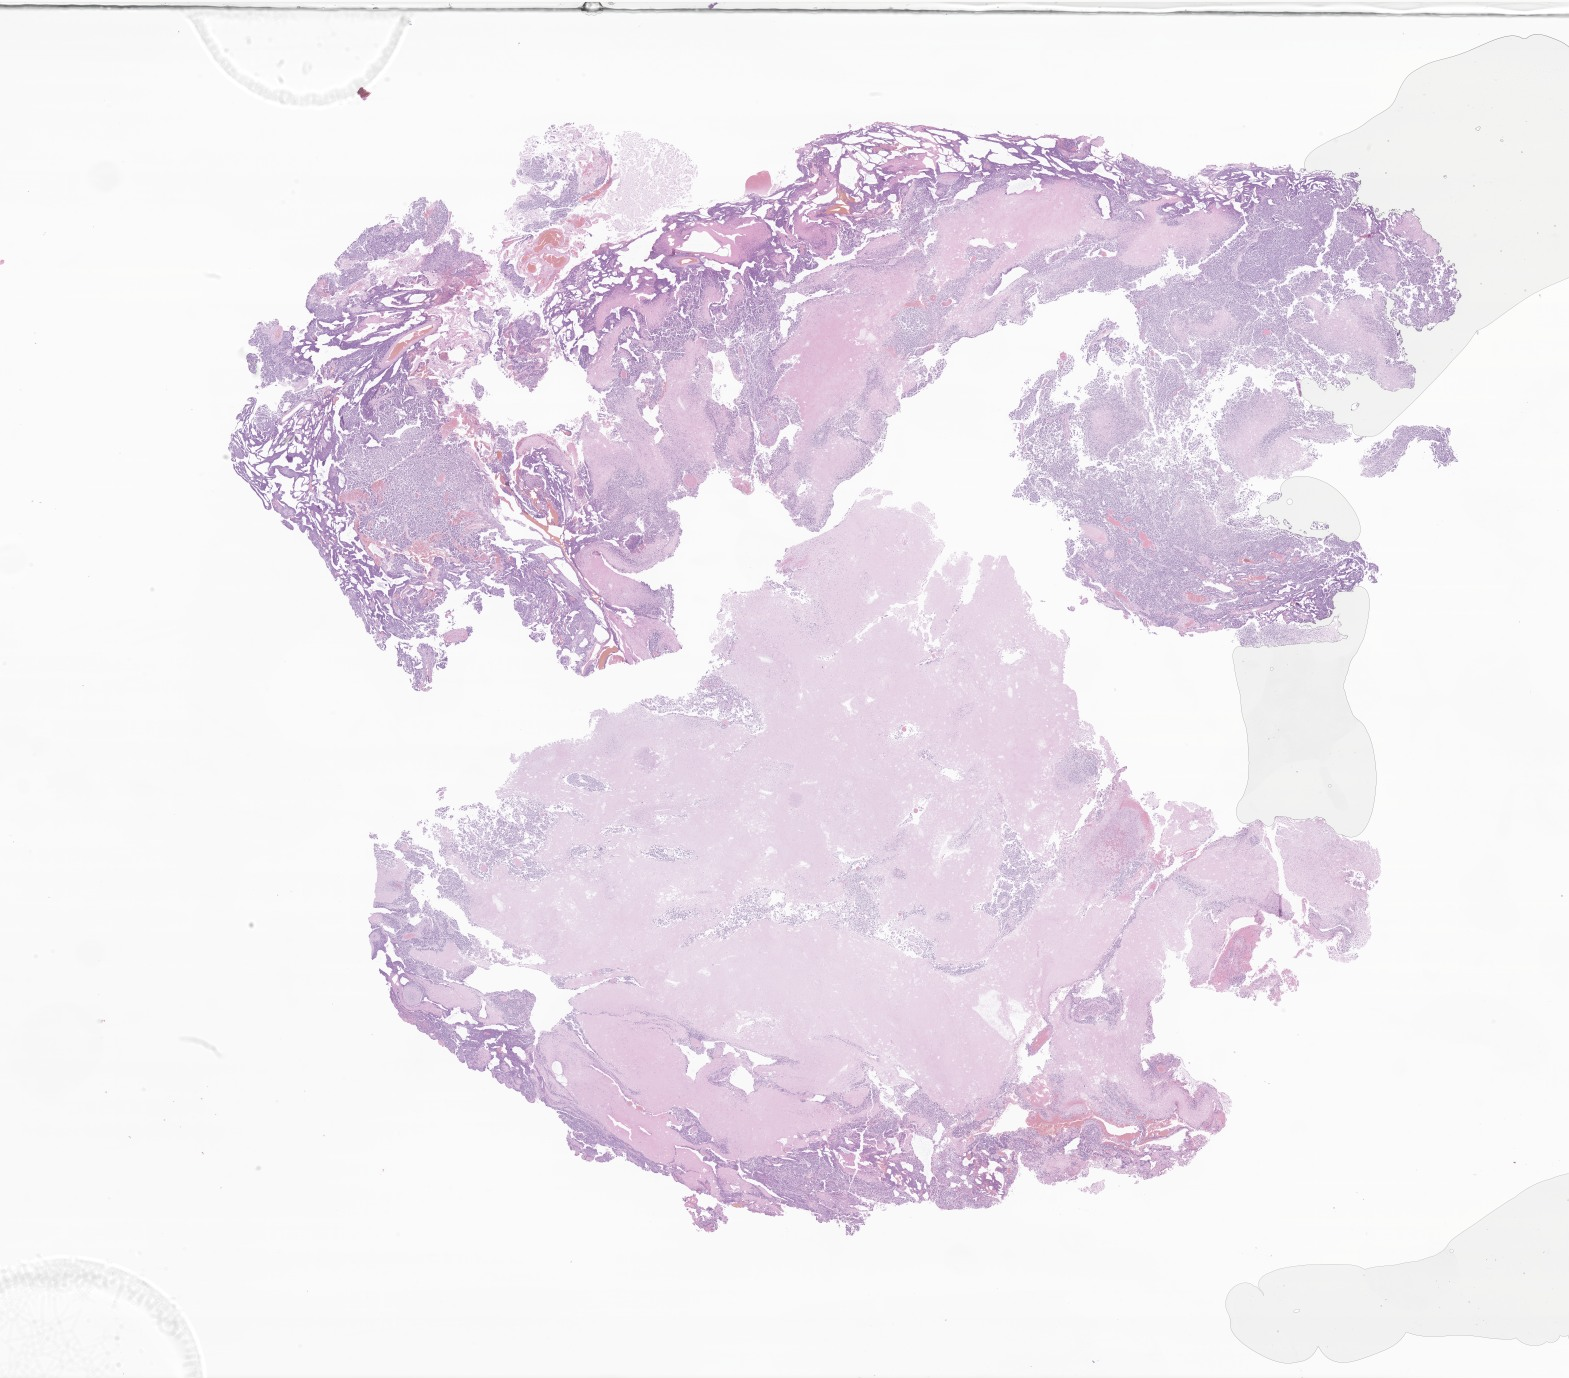
Digitized H&E-stained section of tumor tissue from the brain — a low-resolution overview of the entire scanned area, about 26.5 x 23.2 mm. Formalin-fixed paraffin-embedded section. Female patient, age 243 months (20 years 3 months).
• diagnosis: Medulloblastoma, NOS